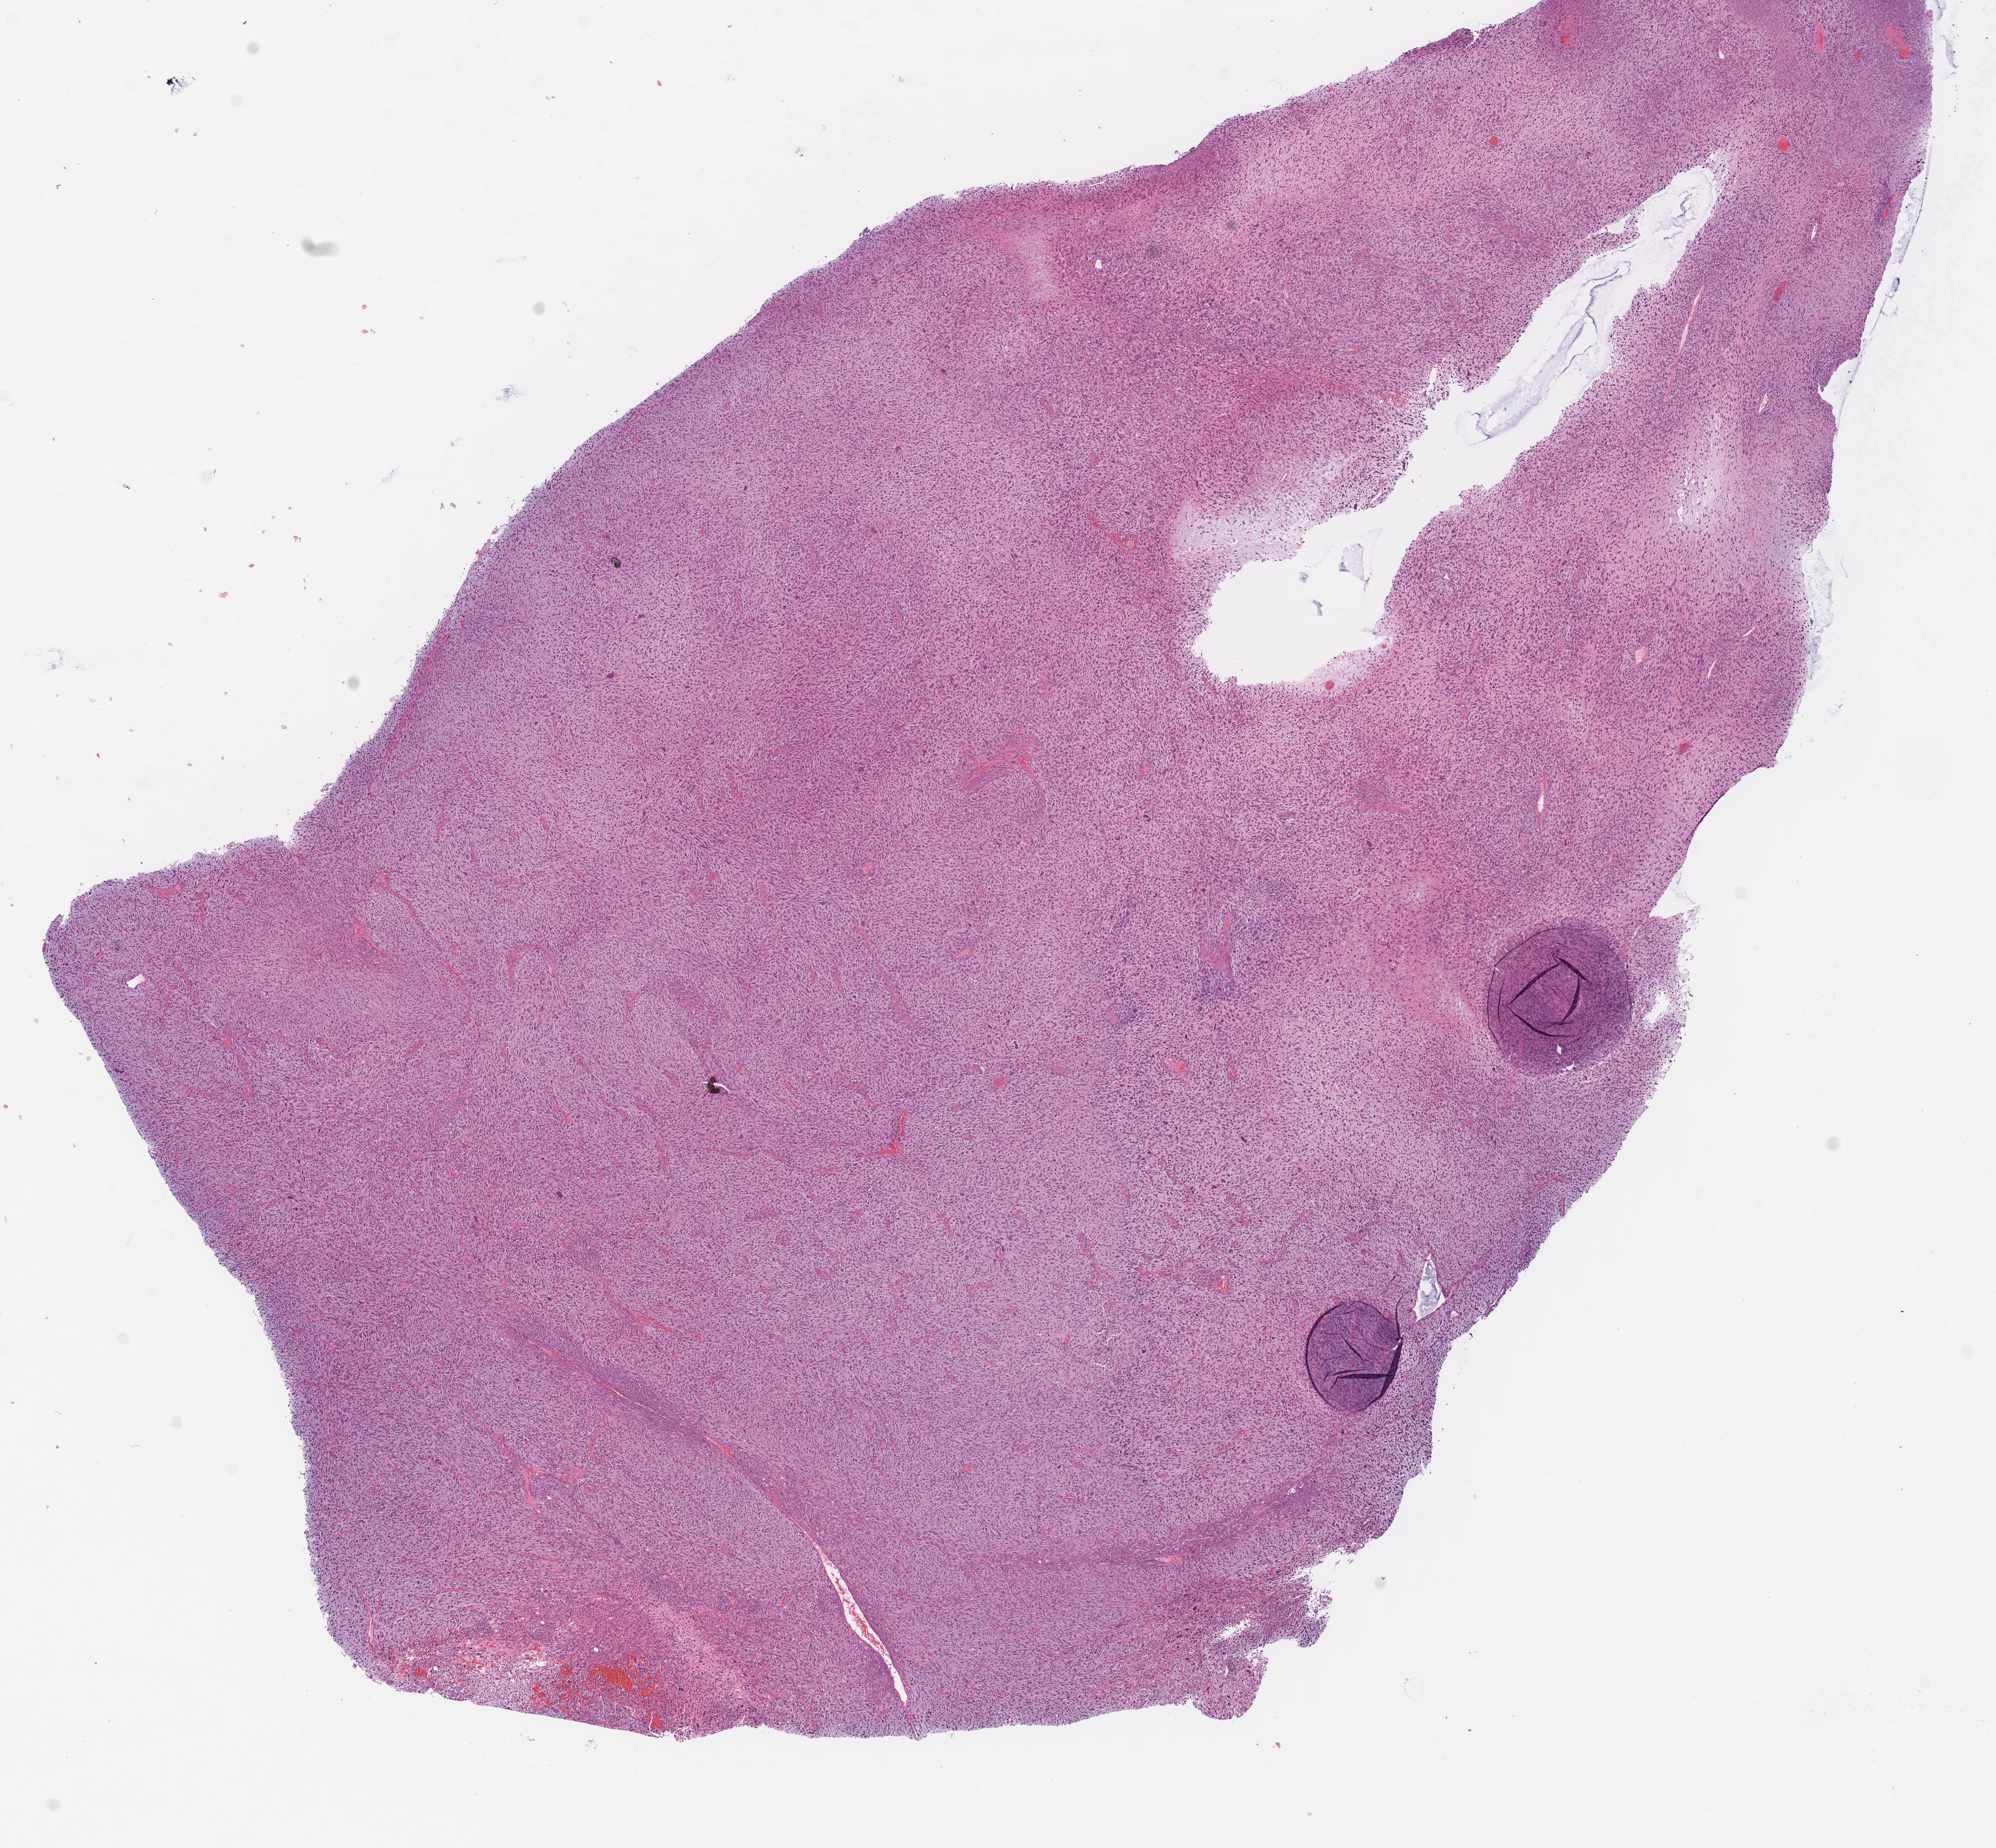
H&E-stained whole-slide image — whole scanned area (about 12.9 x 11.9 mm) shown as a low-resolution overview, formalin-fixed paraffin-embedded (FFPE) diagnostic section, primary tumour sample from the retroperitoneum and peritoneum. Female, age 61 years at initial diagnosis.
Histologic diagnosis: Dedifferentiated liposarcoma (retroperitoneum).